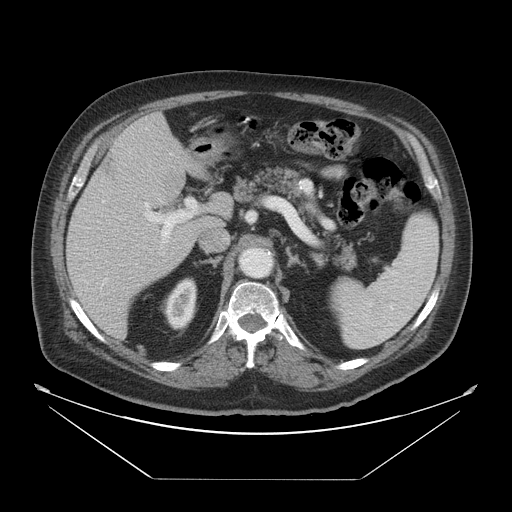
Contrast-enhanced abdominal CT, one axial slice. Slice 30 of 45 in the series (ordered by position). Intravenous contrast given. Soft-tissue window (W 400 / L 40 HU). 5 mm slice thickness. 512 × 512 image matrix, field of view 463 × 463 mm. Male patient, age 87 years. Case-level facts recorded for this patient, not image findings: diagnosis: colorectal cancer liver metastases, imaged before liver resection; multiple liver metastases: no; largest metastasis: 4.5 cm; chemotherapy before resection: no.
Annotated regions visible in this slice (expert manual segmentation):
- liver: bounding box [x1, y1, x2, y2] px = [66, 114, 224, 341]
- planned liver remnant (the part of the liver to remain after resection): [120, 114, 196, 163]
- portal vein (with intrahepatic branches): [120, 199, 196, 265]
- liver metastasis: [162, 167, 186, 198]
- liver metastasis: [98, 151, 123, 185]